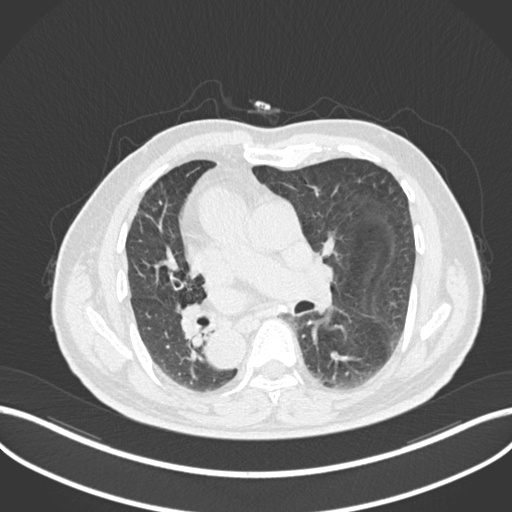
Chest CT, one axial slice; slice 115 of 206 in the series (ordered by position); 120 kVp; lung window (W 1500 / L -600 HU); 1 mm slice thickness; 512 × 512 image matrix, field of view 400 × 400 mm. Male patient, age 67 years. From the clinical record (not read from this slice): clinical TNM (as recorded): T2a N0 M0.
Annotated regions visible in this slice (bounding box drawn by a radiologist):
- lung tumour (recorded histology: squamous cell carcinoma): box from (x=171, y=299) to (x=212, y=344) px